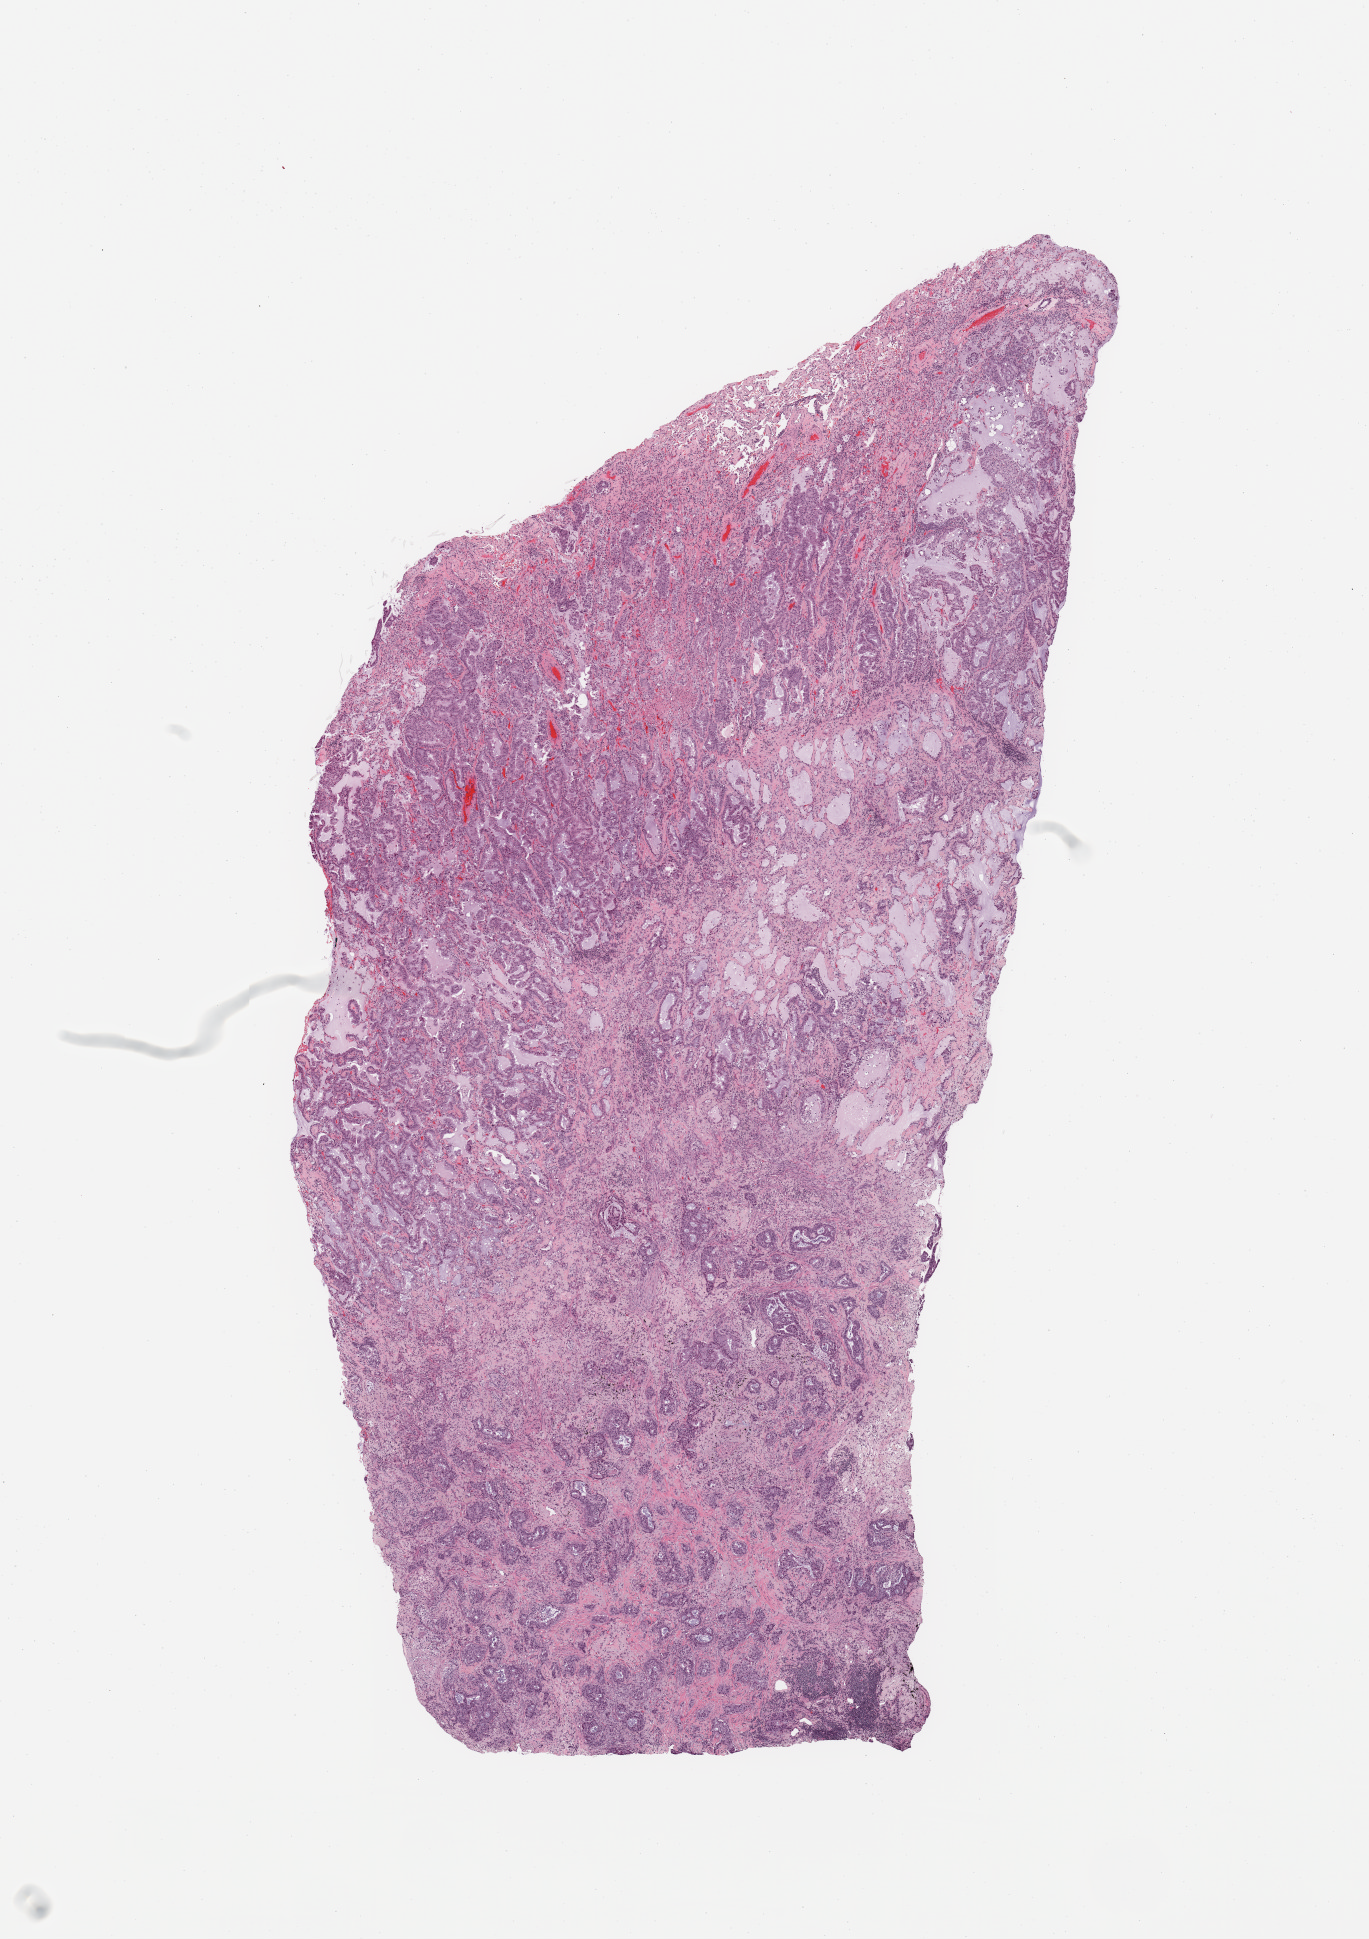
Whole-slide histology image, H&E-stained — low-resolution overview of the scanned area, about 10.8 x 15.3 mm; tumour tissue sample, lung. 60-year-old female patient. Histologic grade: G3 (poorly differentiated).
Primary tumour site (as recorded): right upper lobe. AJCC pathologic stage: IIA. Diagnosis: Adenocarcinoma, NOS.